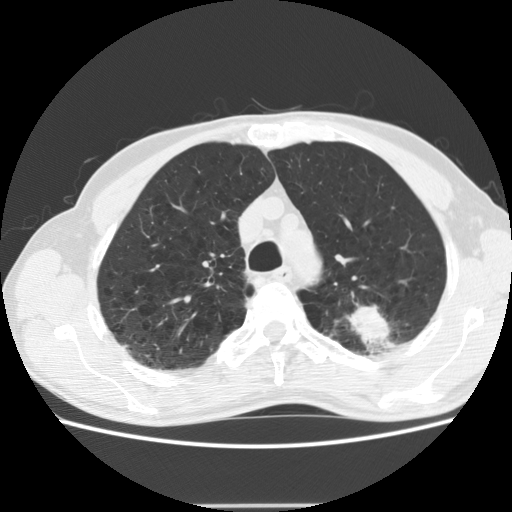
Low-dose screening chest CT, axial slice. First (baseline) screen. Lung window (W 1500 / L -600 HU). 2.5 mm slice thickness. Slice 45 of 191 in the series. Male participant, aged 64 years at enrolment. Current smoker at enrolment.
Expert-annotated lung lesion, bounding box [x1, y1, x2, y2] px = [340, 285, 433, 359]. Reader record for this screening exam (exam-level; its link to the box is not recorded): non-calcified nodule or mass ≥4 mm, left upper lobe, 27 × 19 mm, poorly defined margins, soft tissue attenuation. Participant outcome: lung cancer diagnosed 23 days after this screen — adenocarcinoma, NOS, left upper lobe, moderately differentiated (G2), stage IA (AJCC 6th edition), 29 mm at pathology.